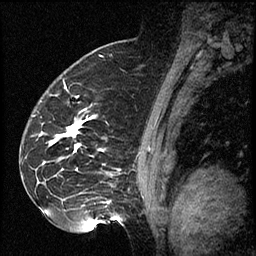
Breast MRI (dynamic contrast-enhanced), one sagittal slice; dynamic contrast-enhanced series, image 2 of 2 at this slice position (ordered by acquisition); 1.5 T; TE 4.2 ms, TR 17.3 ms; 2 mm slice thickness; 256 × 256 image matrix. Female patient. From the clinical record (not read from this slice): setting: breast cancer imaged before/during neoadjuvant chemotherapy; receptor status: HR-positive, HER2-negative.
Outlined on this slice (semi-automatic segmentation, software-assisted and operator-edited):
- analysis volume of interest (the breast-tissue region the enhancement analysis was run in; not a lesion): box from (x=41, y=95) to (x=115, y=223) px
- tumour enhancement mask (voxels above the 100 % enhancement threshold inside the analysis volume of interest): (x=66, y=124)–(x=81, y=152)